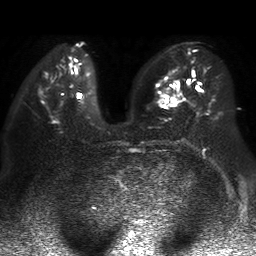
Breast MRI, one axial slice; slice 20 of 50 in the series (ordered by position); diffusion-weighted series; image 2 of 4 stored at this slice position (different b-values; order by instance number); 1.5 T; 4 mm slice thickness; 256 × 256 image matrix, field of view 360 × 360 mm. Female patient.
Outlined on this slice (manually delineated by an expert):
- tumour on diffusion-weighted imaging: bounding box (x1, y1, x2, y2) in pixels: (172, 98, 176, 101)